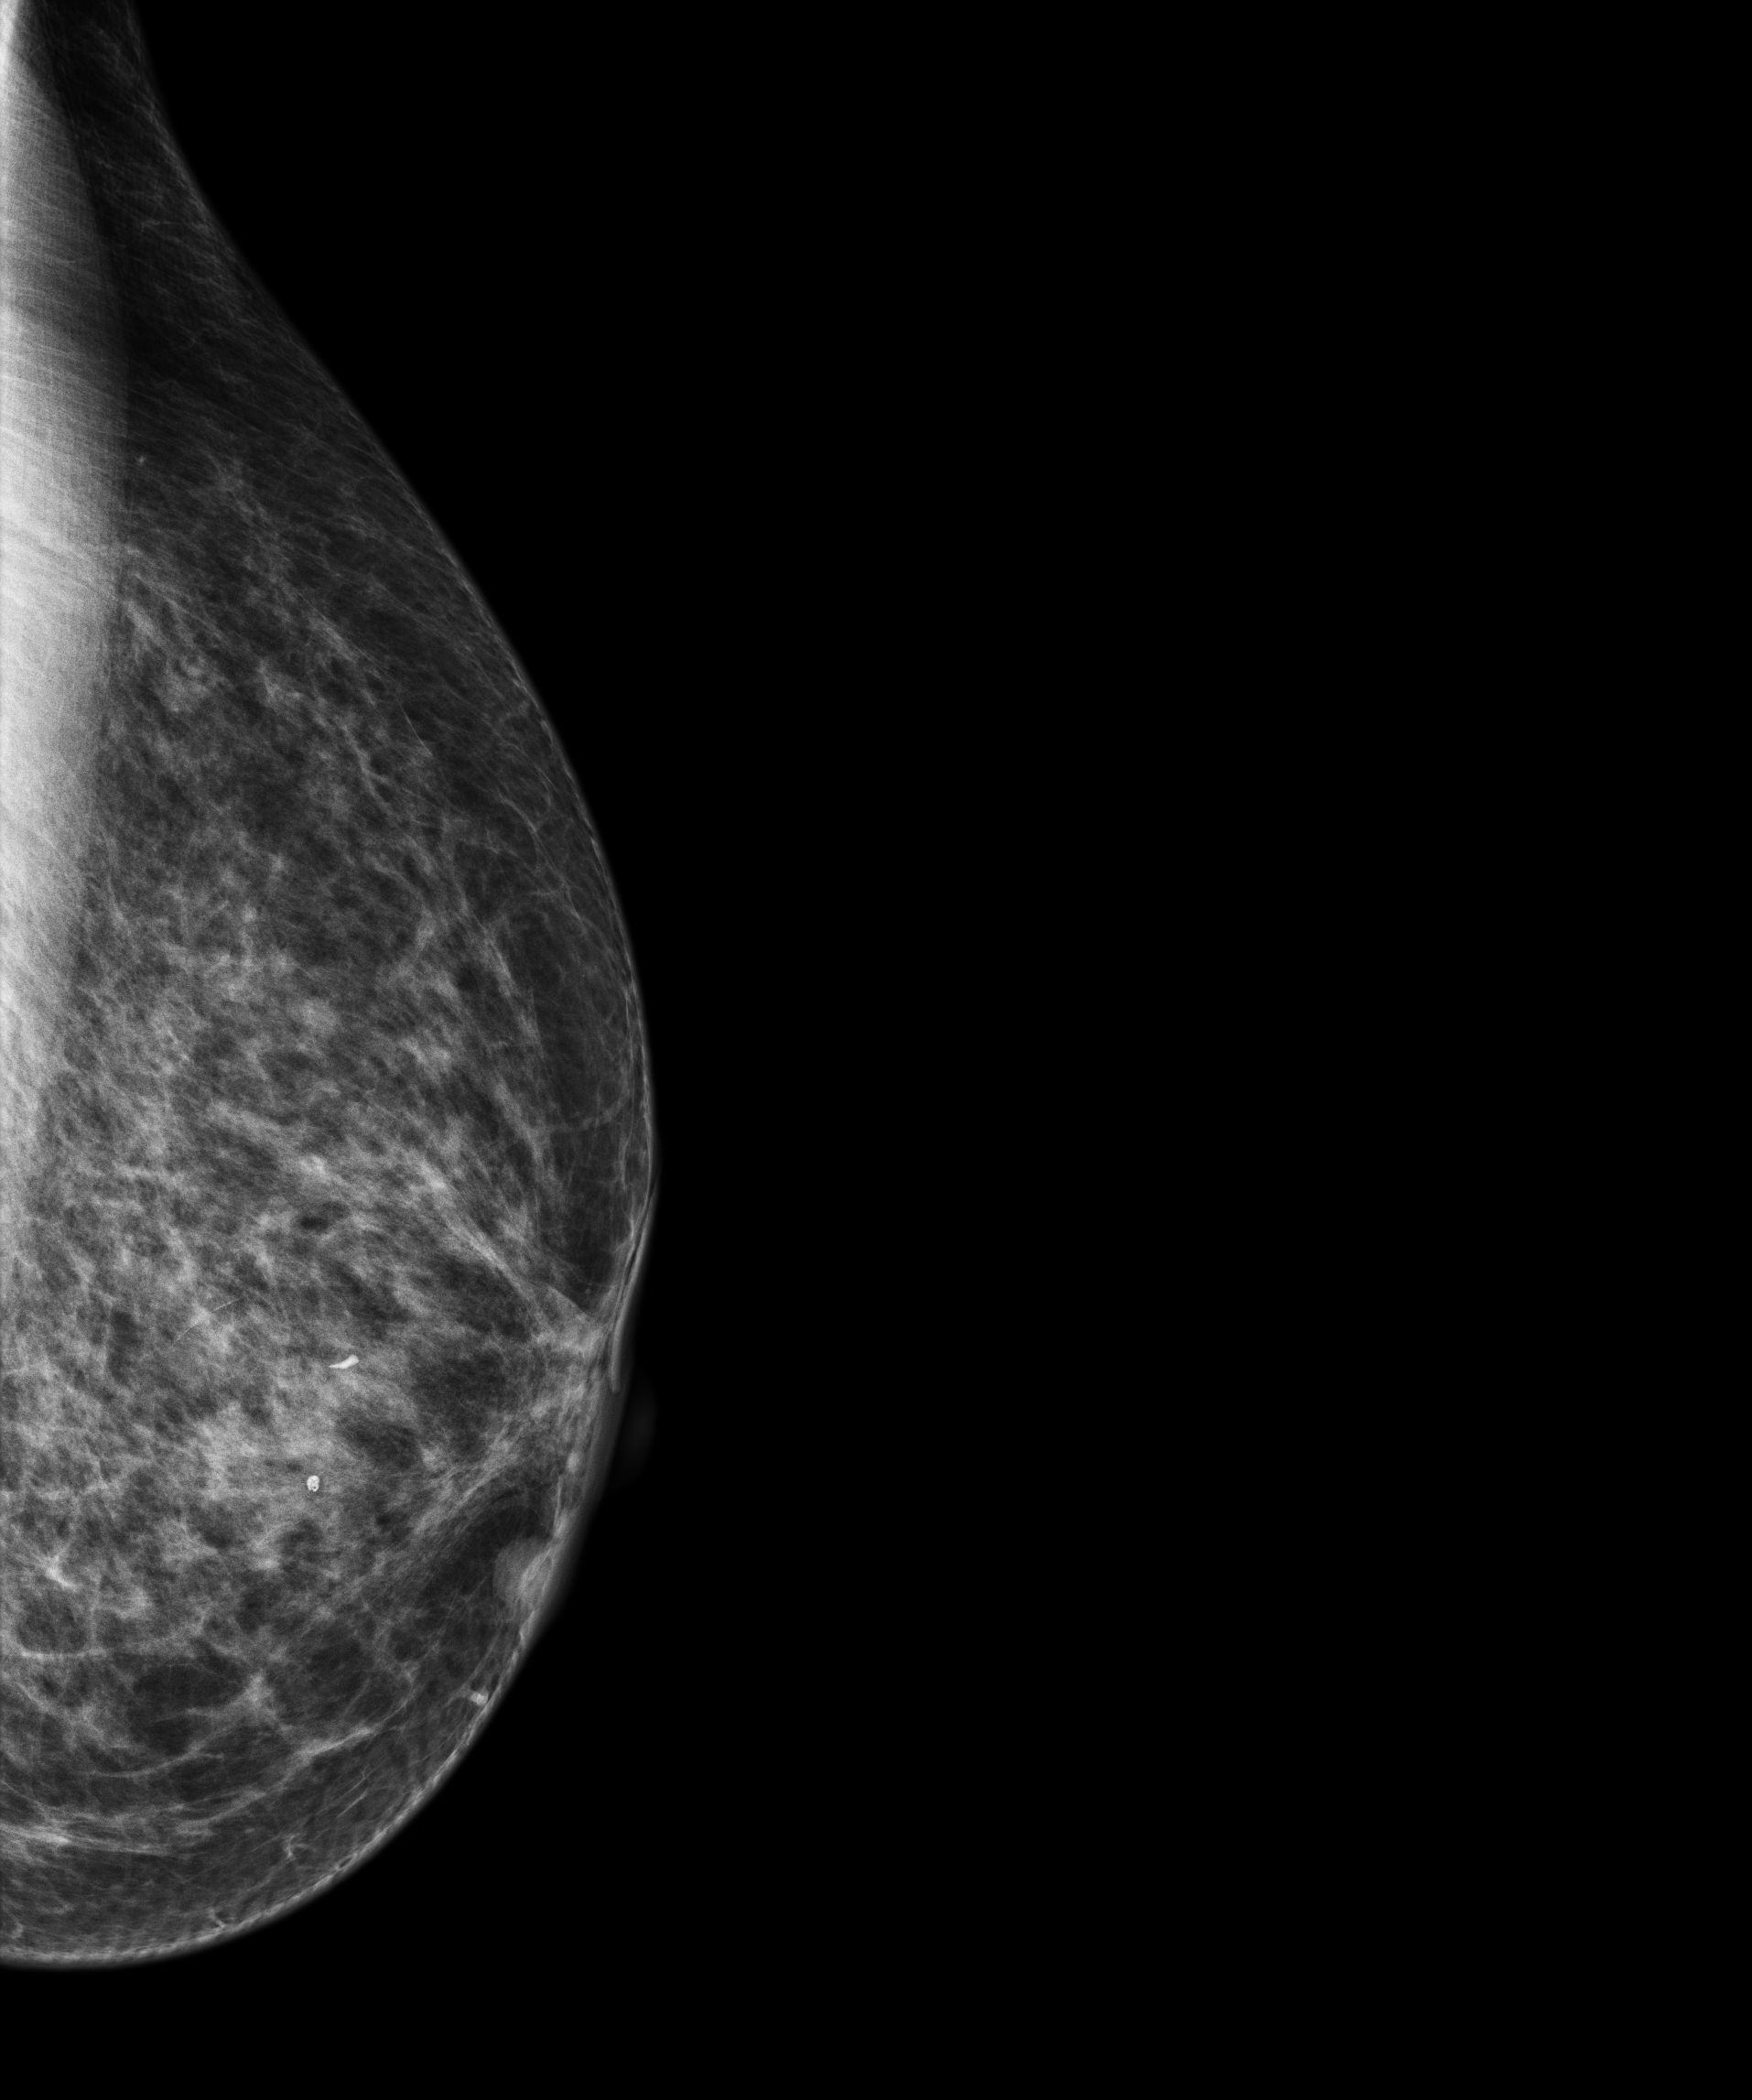
Annual screening mammography examination; compressed breast thickness 60 mm; system: Senographe Essential ADS_56.21.3. Female patient, age 70 years.
Image type: full-field digital mammogram. Breast: left. Projection: exaggerated CC view (lateral).